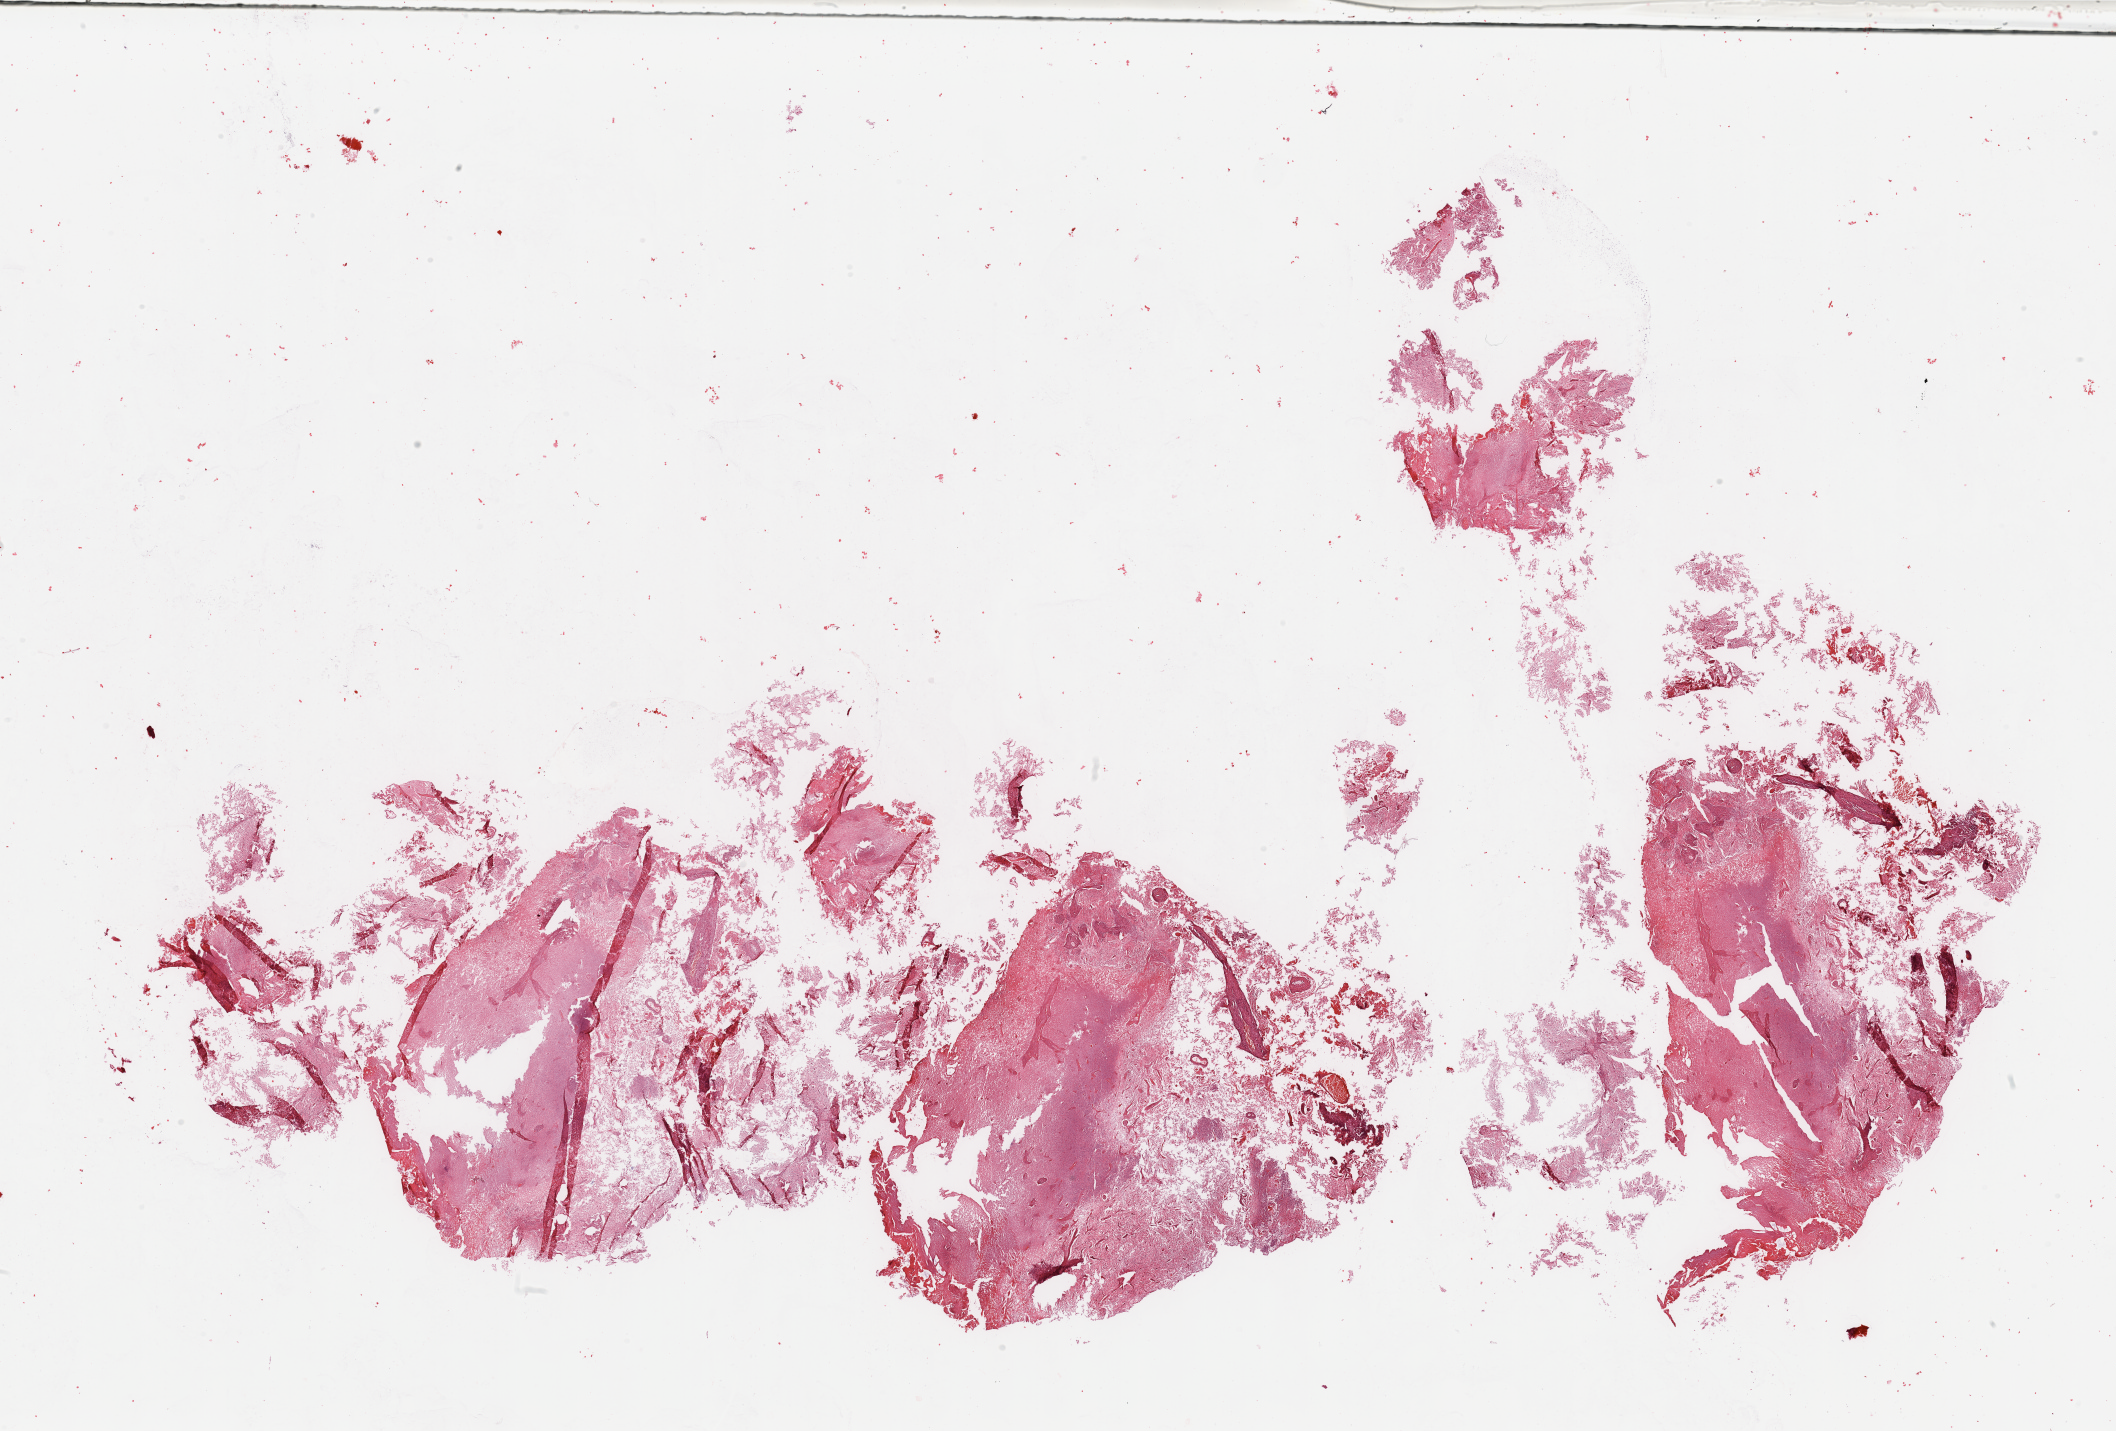
Digitized H&E tissue section (whole slide) — whole scanned area (about 33.5 x 22.6 mm, from a 20x scan) shown as a low-resolution overview. Tumour tissue sample, sampled site: frontal lobe. Patient: female, age 65 years. Slide review estimates, as recorded: tumour nuclei 60%, necrosis 45%.
Primary tumour site (as recorded): frontal lobe. Diagnosis: Glioblastoma.